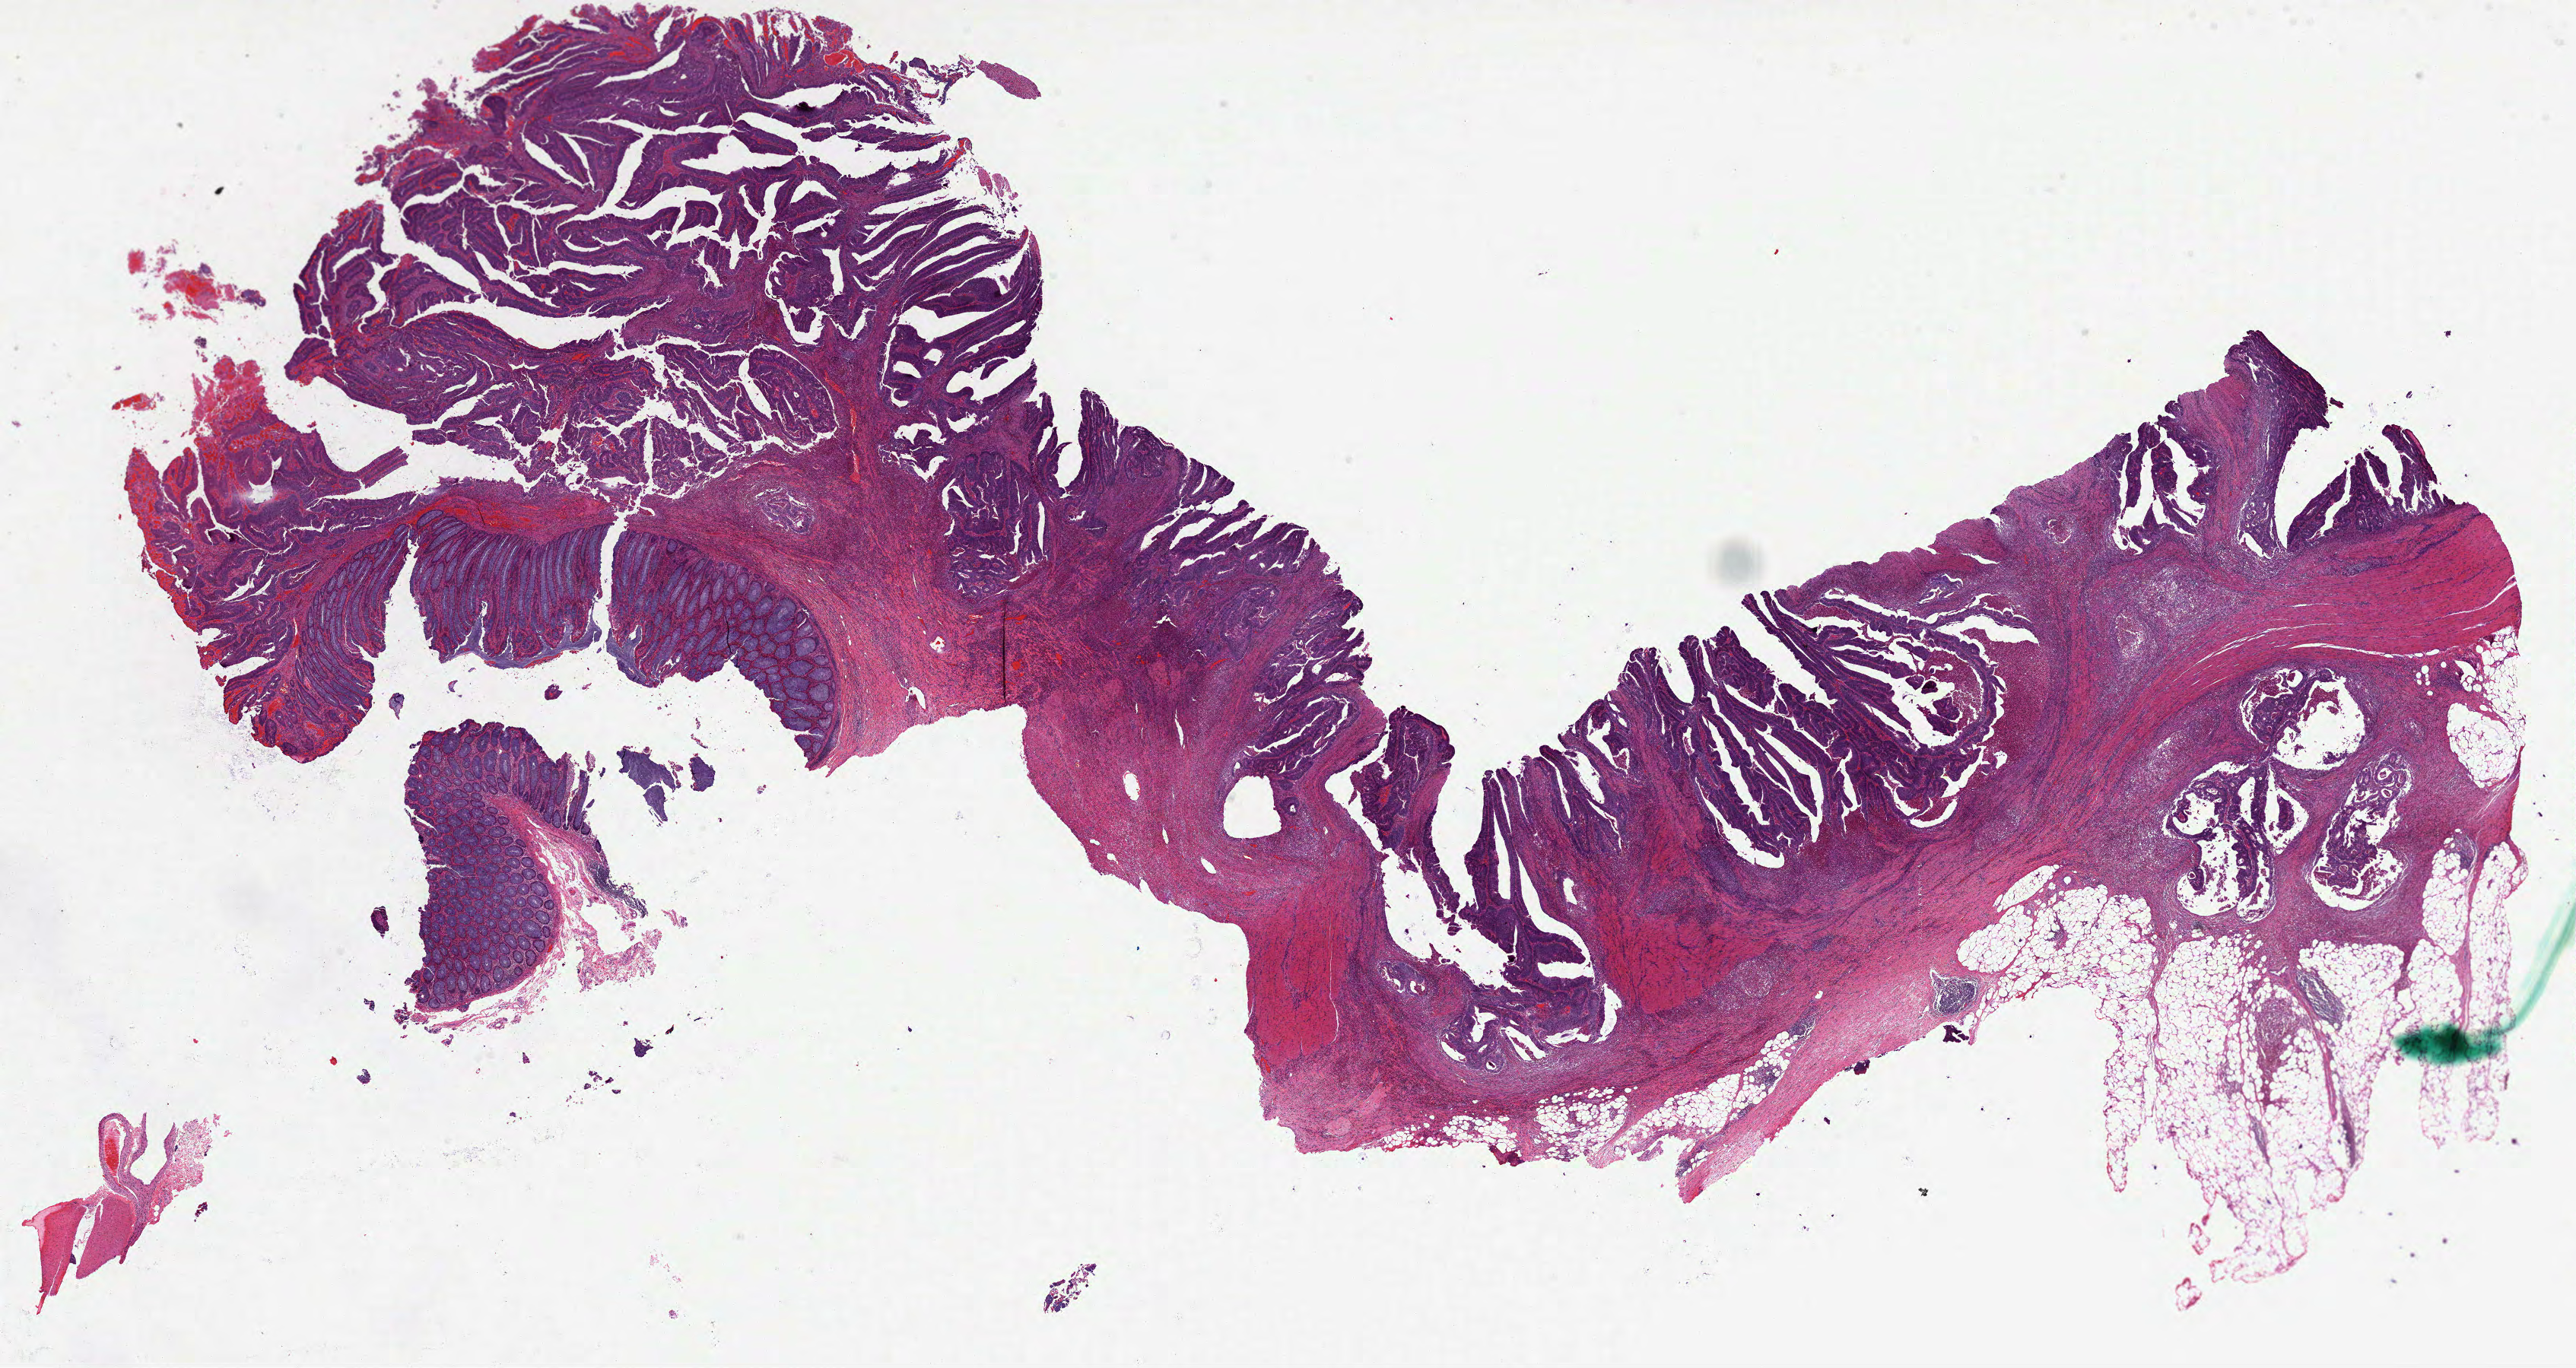
Hematoxylin and eosin (H&E) stained whole-slide image — shown as a low-resolution overview of the whole scanned area (about 27.3 x 14.5 mm, from a 40x scan). FFPE section. Sample: primary tumour, rectum. Male, age 57 years at initial diagnosis.
- AJCC pathologic stage: IIA (7th edition)
- diagnosis: Adenocarcinoma, NOS (rectosigmoid junction)